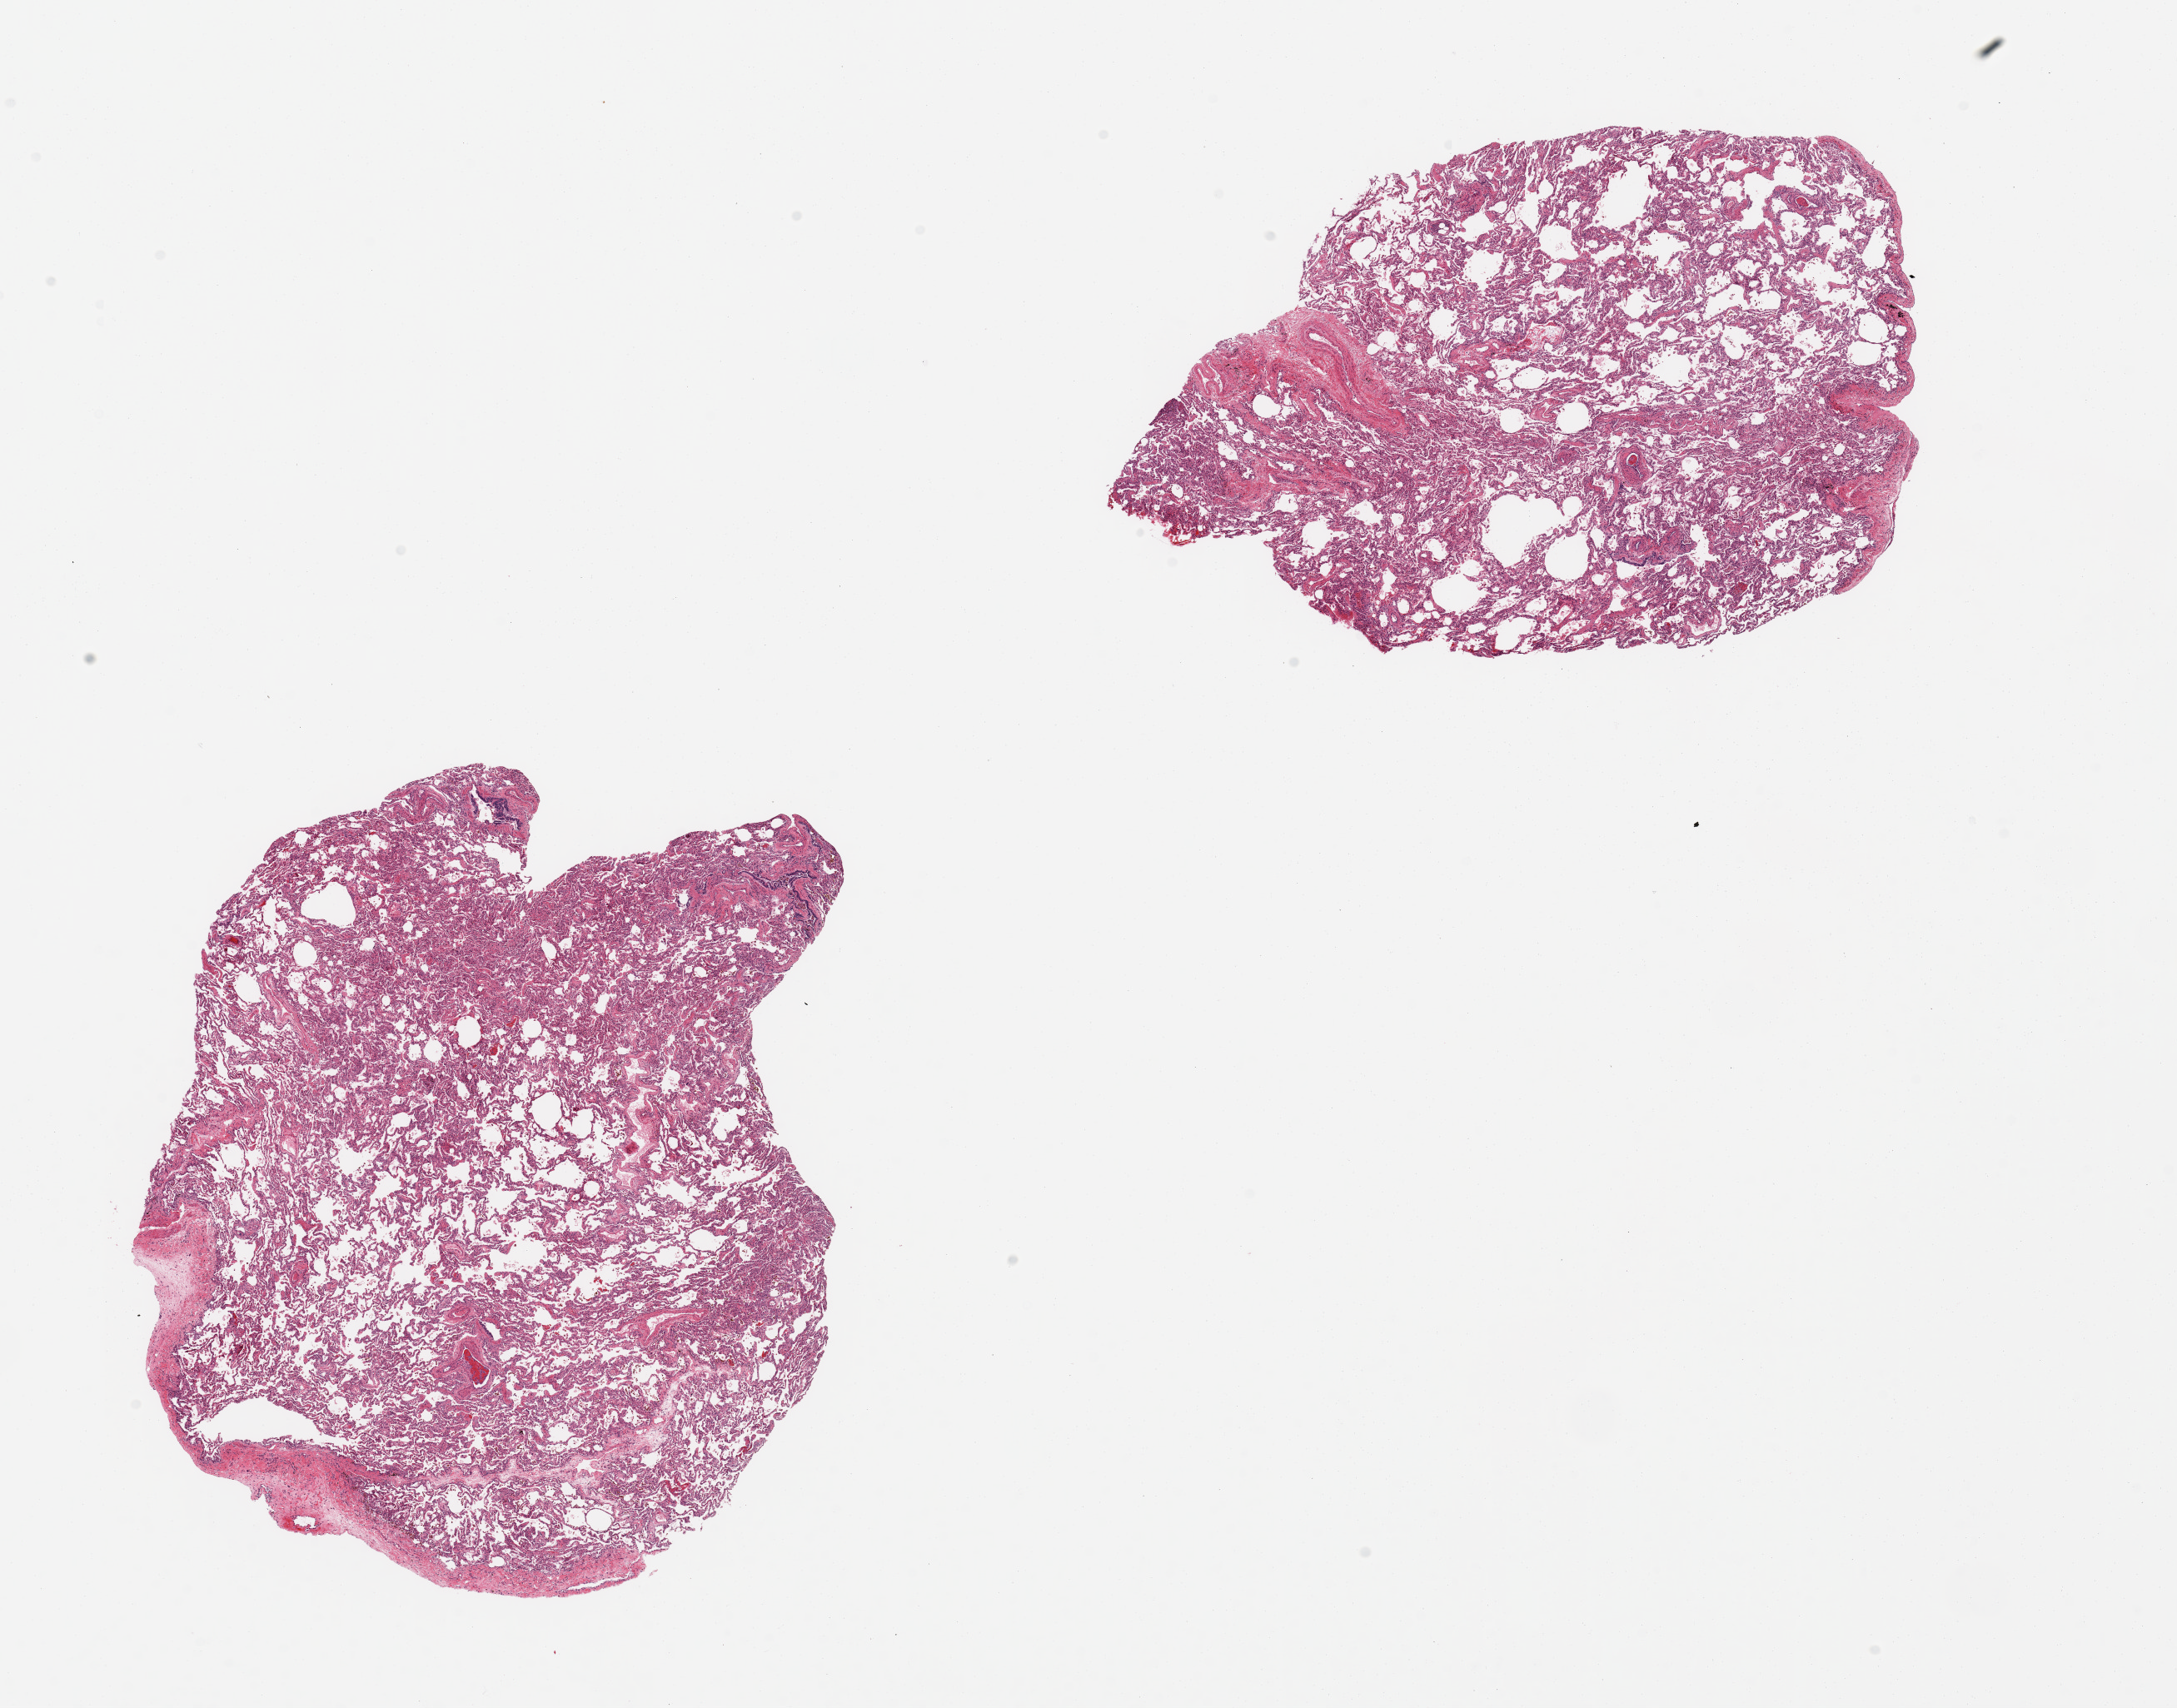
H&E whole-slide image — shown as a low-resolution overview of the whole scanned area (about 20.7 x 16.2 mm). PAXgene-fixed, paraffin-embedded tissue. Sampled site (target tissue): lung. Tissue donor sample. Donor: female.
Review note (as recorded): 2 pieces chronic interstitial pneumonitis.